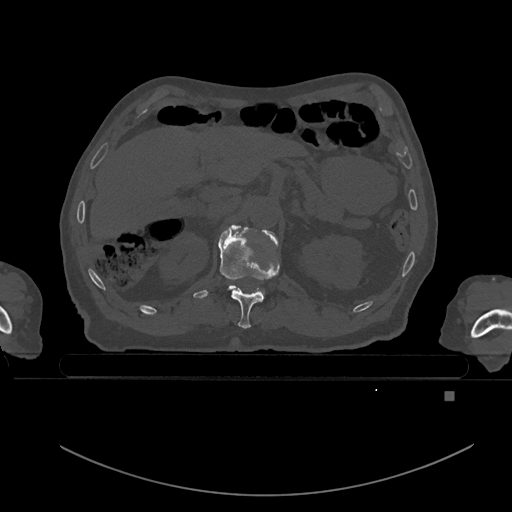
CT including the spine, one axial slice. Bone window (W 1800 / L 400 HU). 0.5 mm slice thickness. 512 × 512 image matrix. Male patient, age 82 years. From the clinical record (not read from this slice): primary cancer: prostate; vertebrae with lytic lesions (as recorded): T11, T9, T8, T2.
Outlined on this slice (semi-automatic segmentation, software-assisted and operator-edited):
- T11 vertebra: bounding box <218,227,280,329> (left, top, right, bottom; pixels)